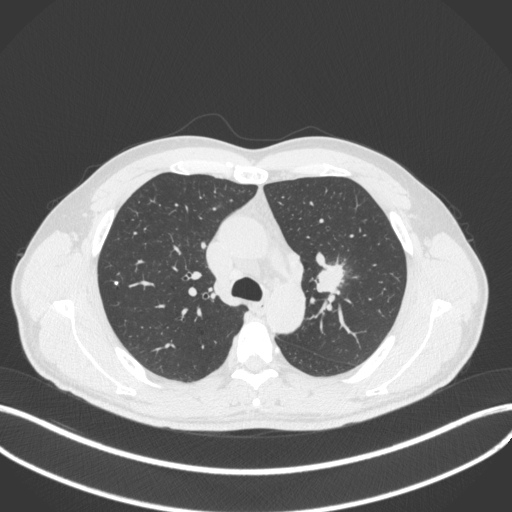
Chest CT, one axial slice; reconstruction kernel B31f; lung window (W 1500 / L -600 HU); 1 mm slice thickness; 512 × 512 image matrix, field of view 400 × 400 mm. Male patient, age 50 years. Case-level facts recorded for this patient, not image findings: clinical TNM (as recorded): T1c N1 M1b.
Annotated regions visible in this slice (bounding box drawn by a radiologist):
- lung tumour (recorded histology: squamous cell carcinoma): bounding box [x1, y1, x2, y2] px = [311, 252, 347, 297]